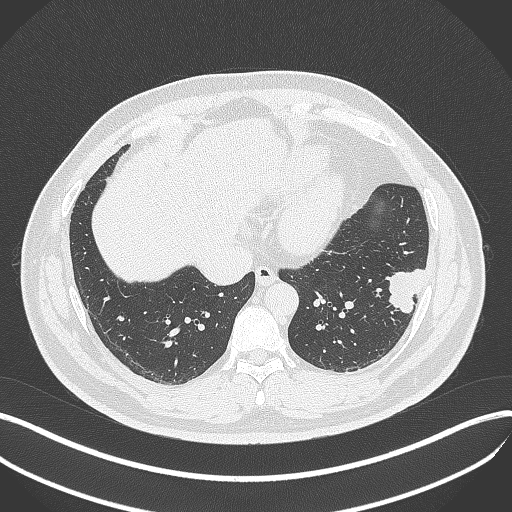
Chest CT, one axial slice. Slice 131 of 429 in the series (ordered by position). Reconstruction kernel B70f. Lung window (W 1500 / L -600 HU). 1 mm slice thickness. 512 × 512 image matrix, field of view 400 × 400 mm. Patient: male, 39 years. From the clinical record (not read from this slice): clinical TNM (as recorded): T2a N0 M0; histopathological grade: G2-3.
Structures marked on this image (bounding box drawn by a radiologist):
- lung tumour (recorded histology: adenocarcinoma): box from (x=383, y=268) to (x=430, y=315) px